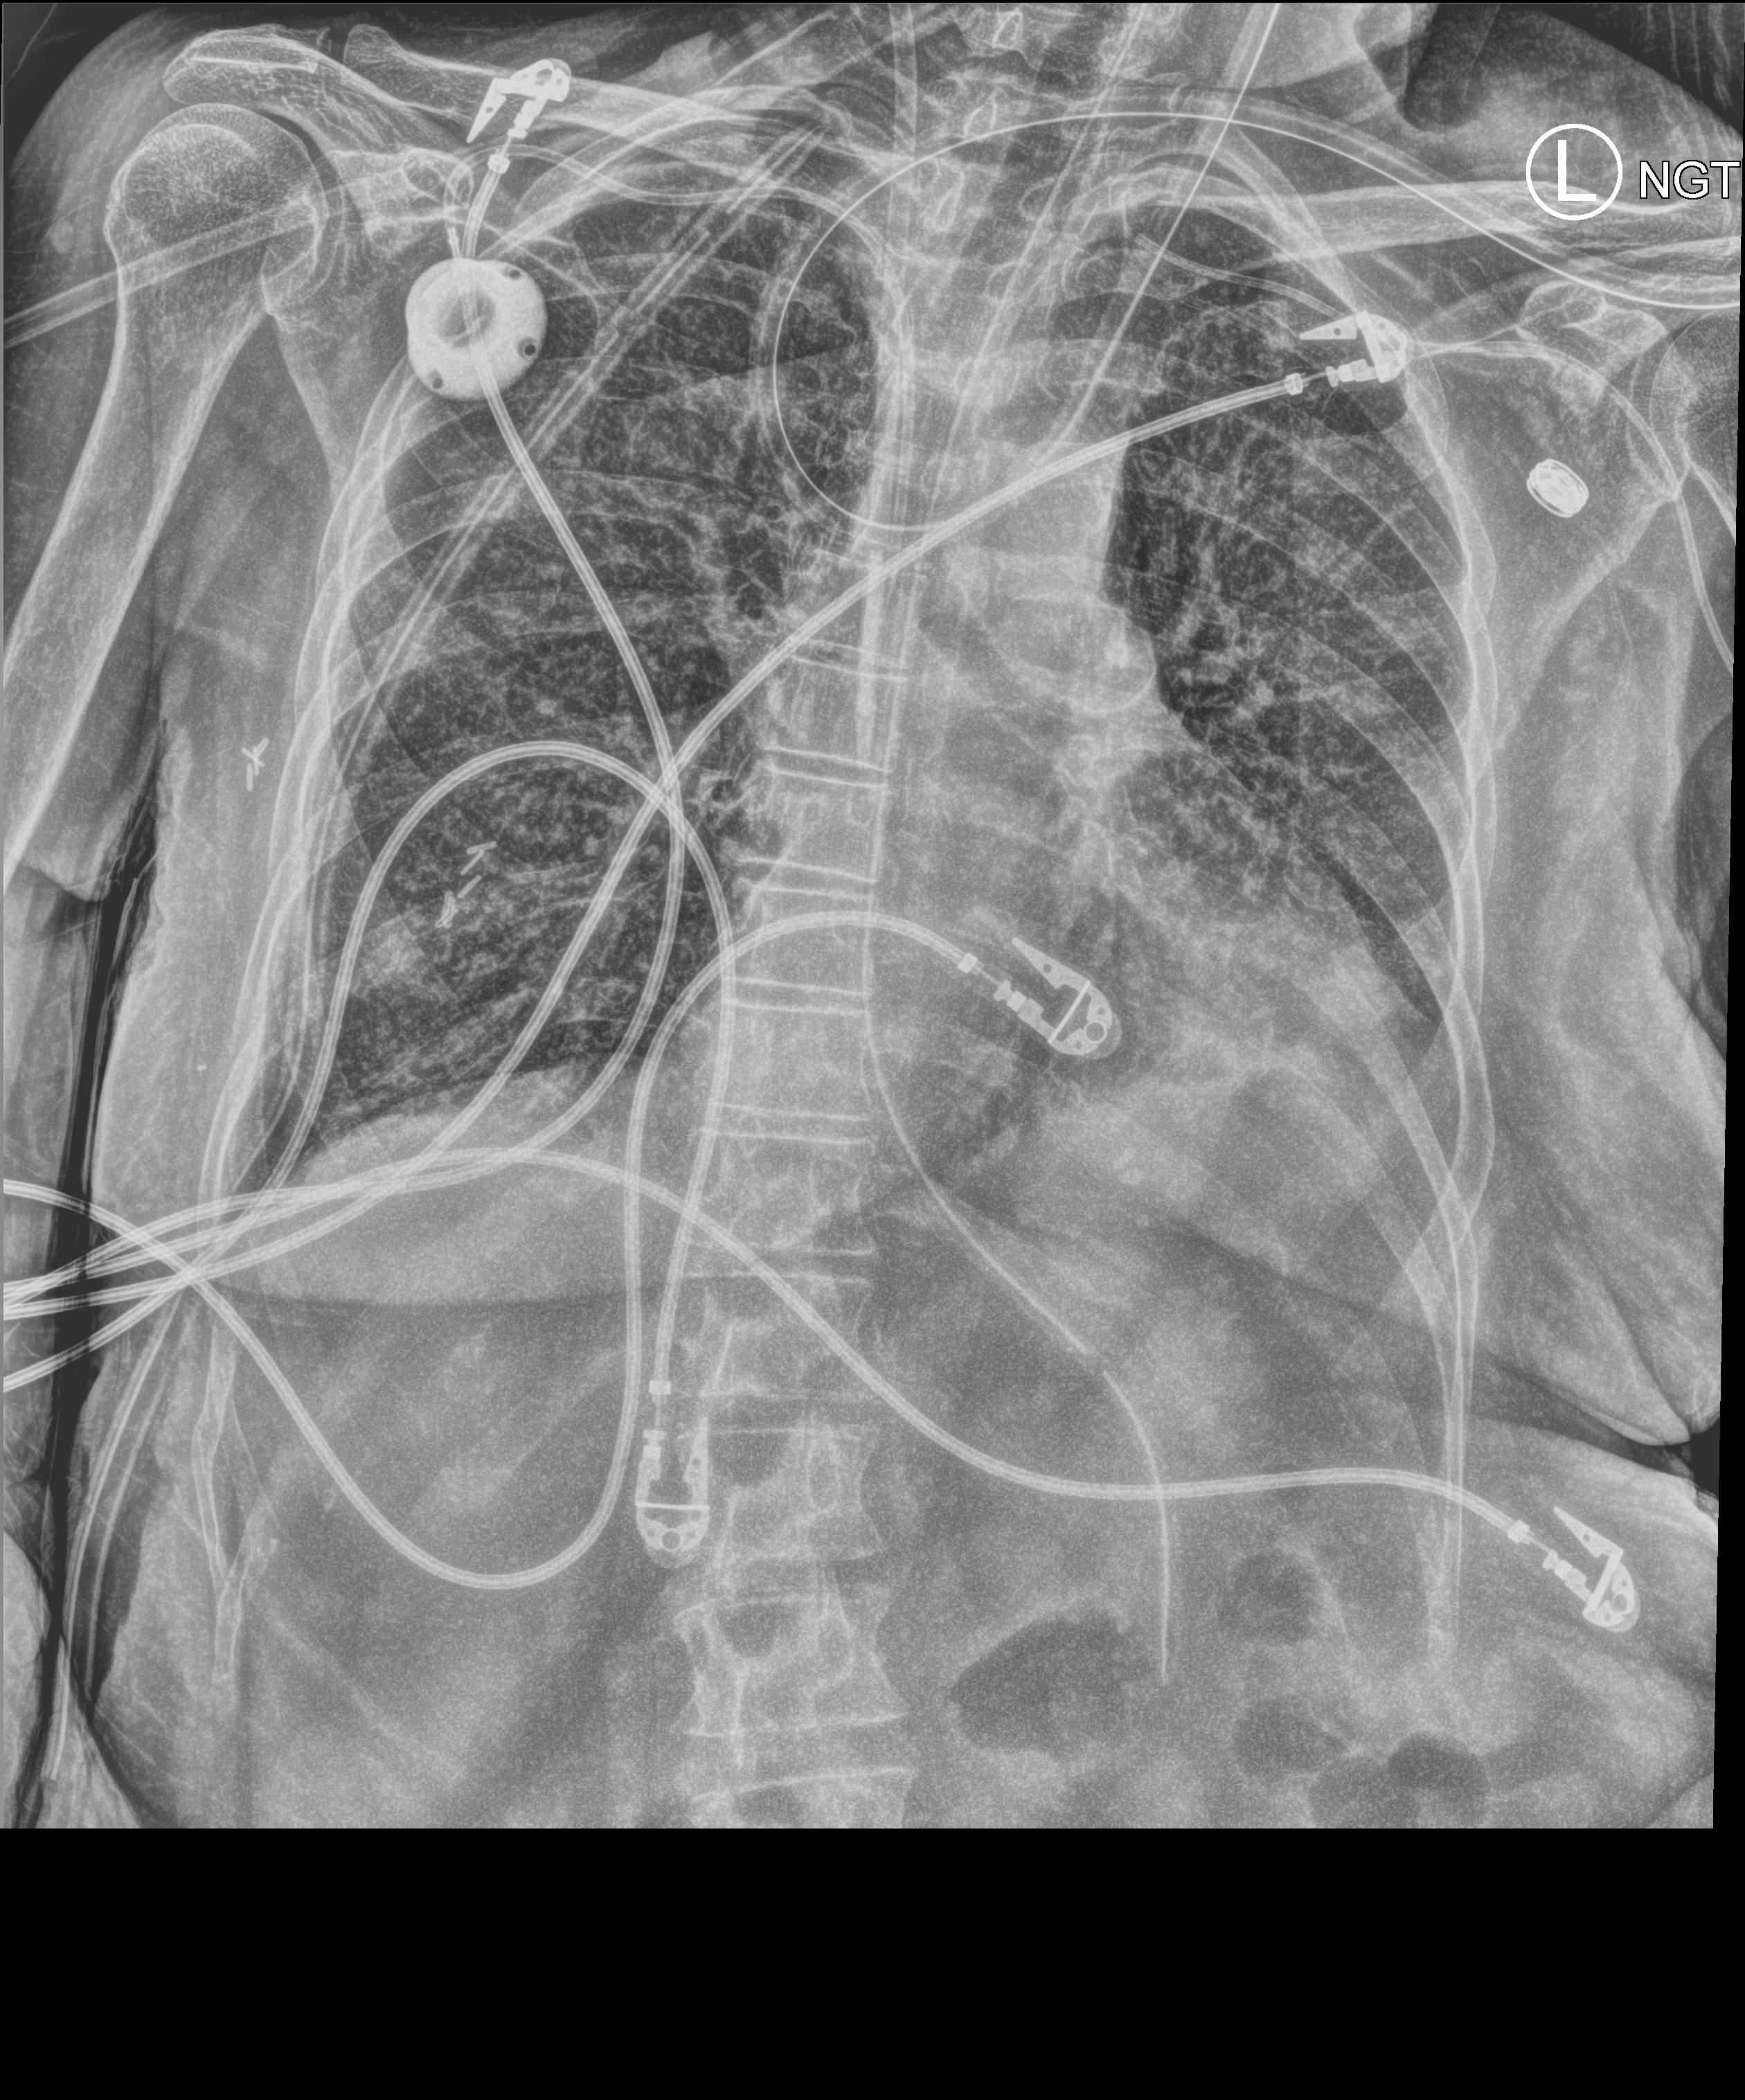
Portable chest radiograph, anteroposterior (AP) projection. Patient hospitalised with COVID-19; female, aged 60–74 years.
From the hospital-stay record, not from the radiograph (when in the stay this image was taken is not recorded):
- admitted to intensive care during this hospital stay: yes